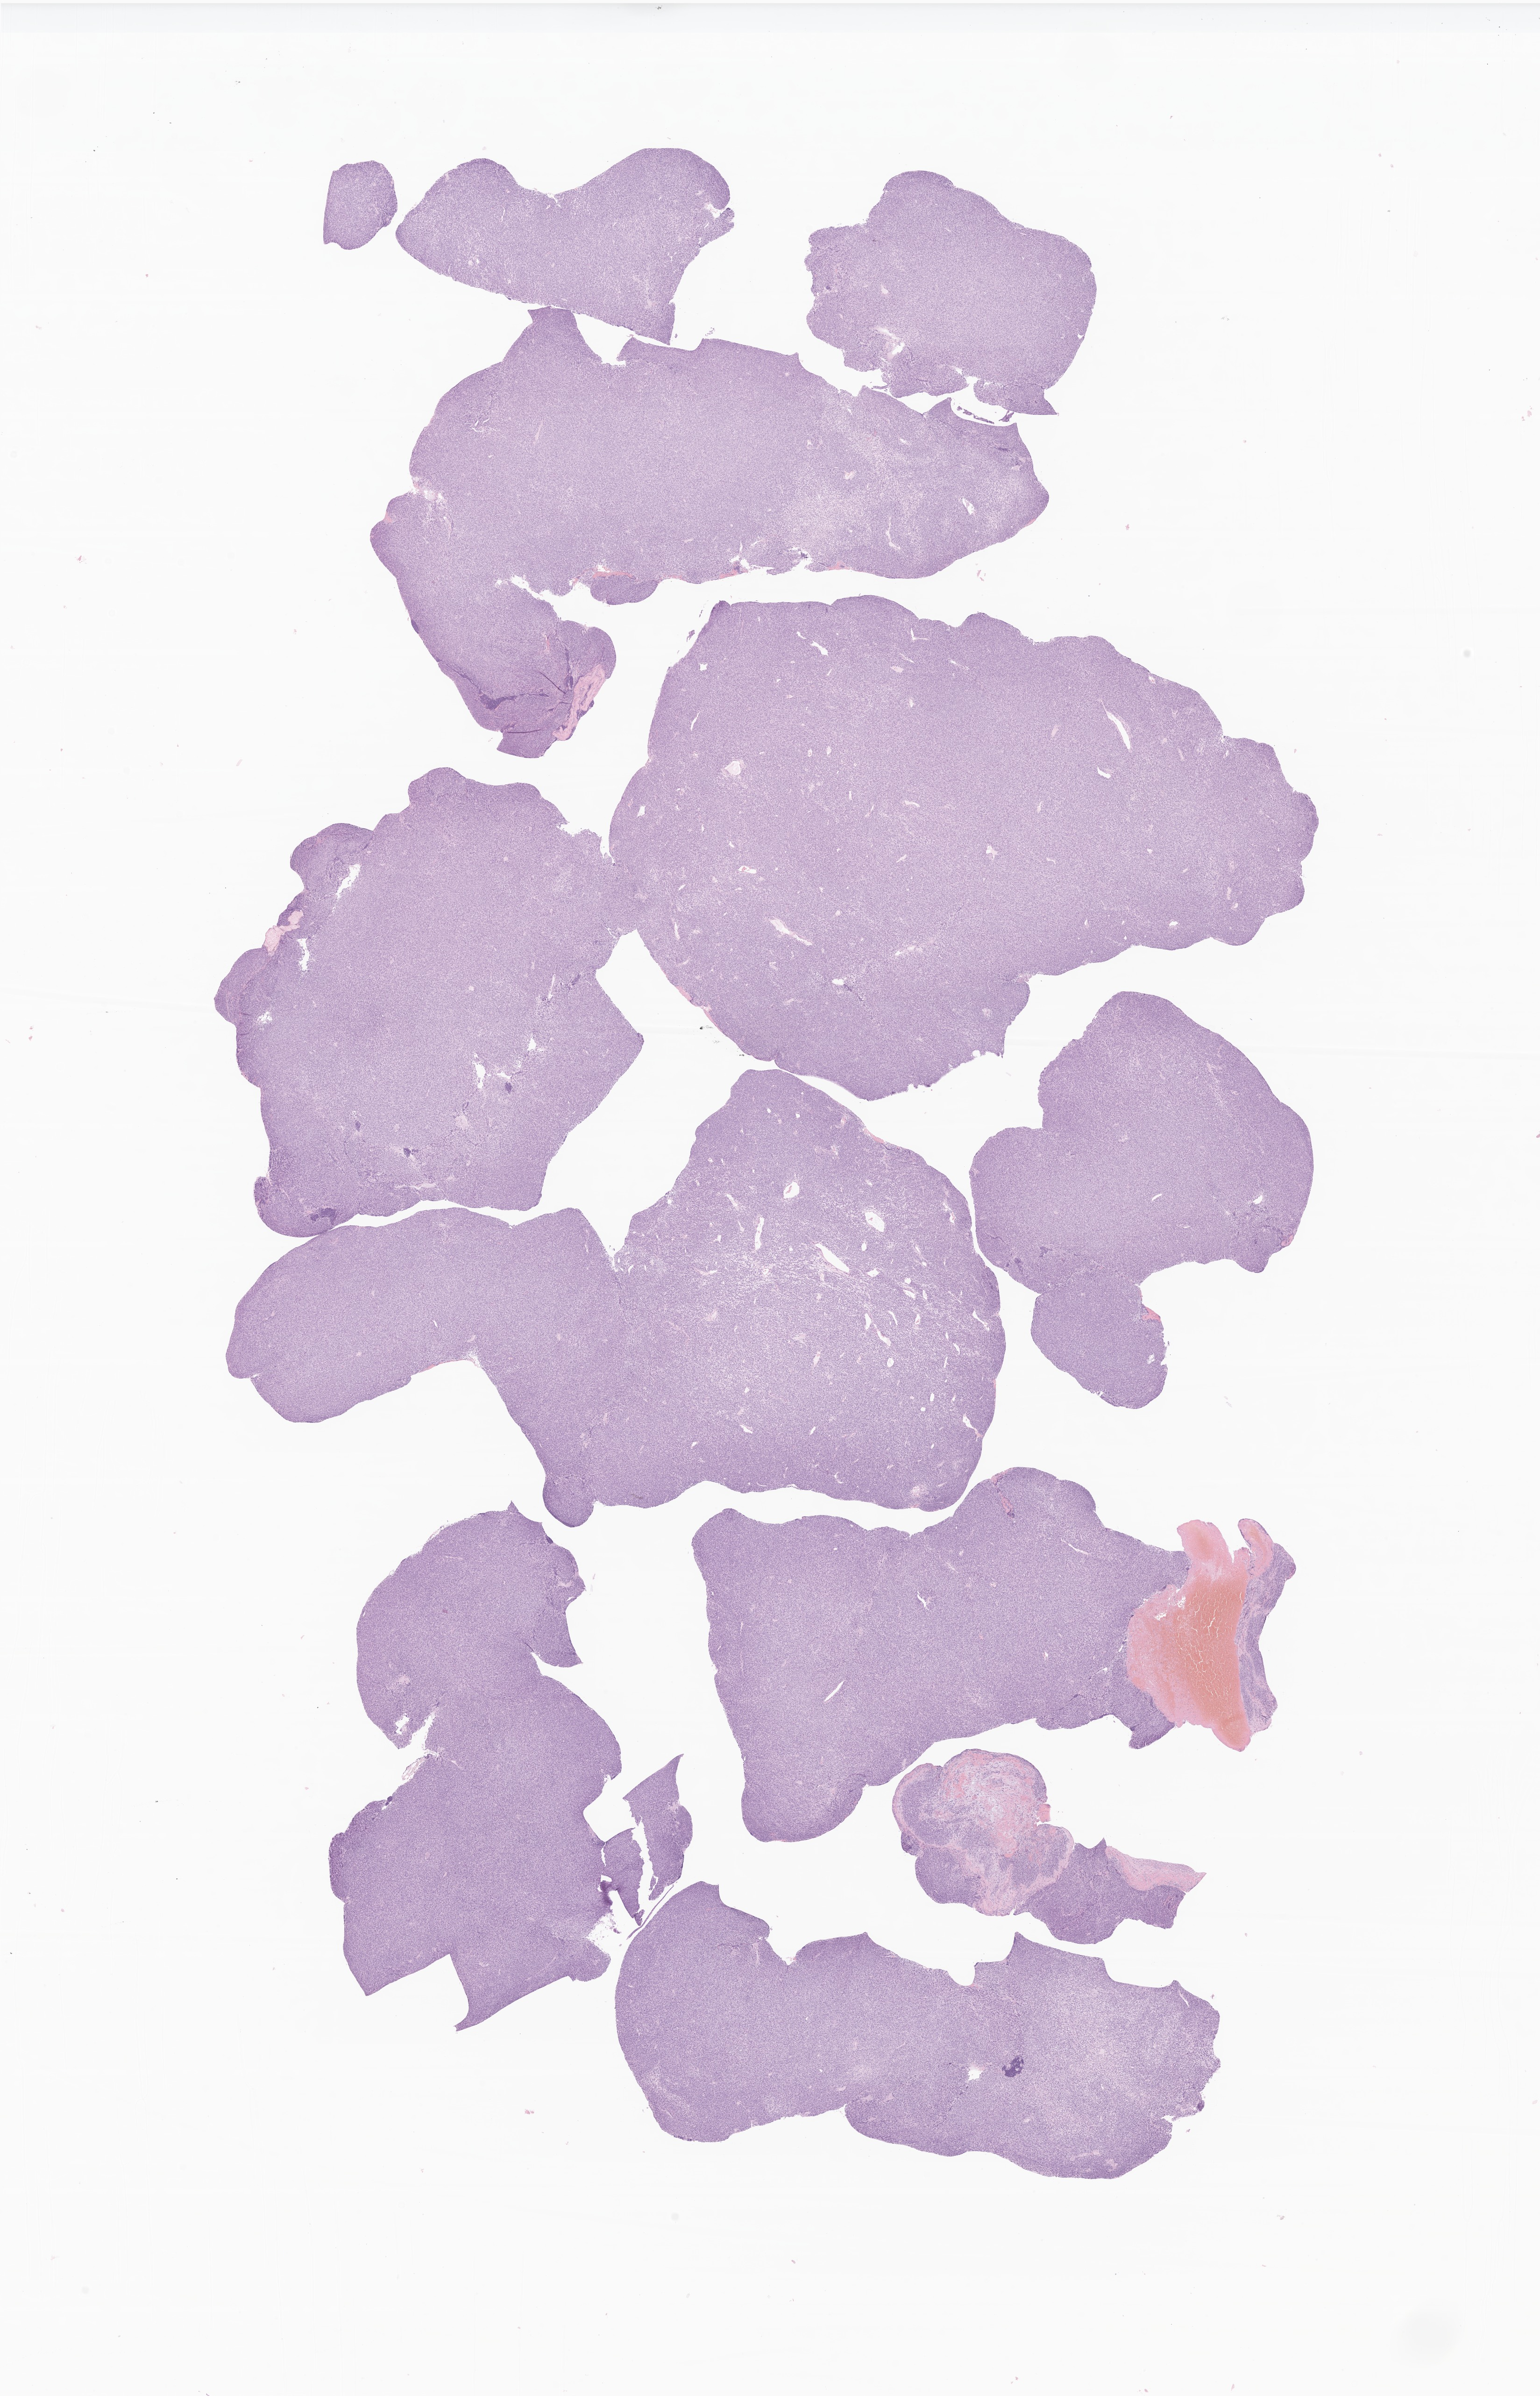
Whole-slide image, hematoxylin and eosin (H&E) stain of tumor tissue from the abdomen, shown as a low-resolution overview of the whole scanned area (about 13.9 x 21.6 mm); FFPE section. Male patient, age 55 months (4 years 7 months).
* recorded diagnosis: Embryonal rhabdomyosarcoma, NOS